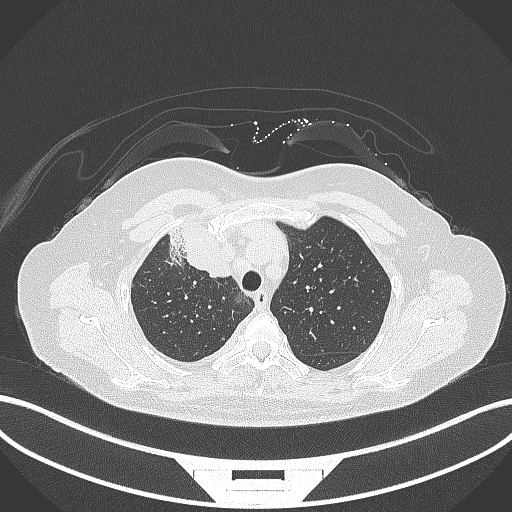
Chest CT, one axial slice. Slice 240 of 305 in the series (ordered by position). 120 kVp. Lung window (W 1500 / L -600 HU). 1 mm slice thickness. 512 × 512 image matrix. Female patient, age 52 years. From the clinical record (not read from this slice): clinical TNM (as recorded): T3 N1 M1.
Outlined on this slice (bounding box drawn by a radiologist):
- lung tumour (recorded histology: adenocarcinoma): bounding box <165,221,239,280> (left, top, right, bottom; pixels)